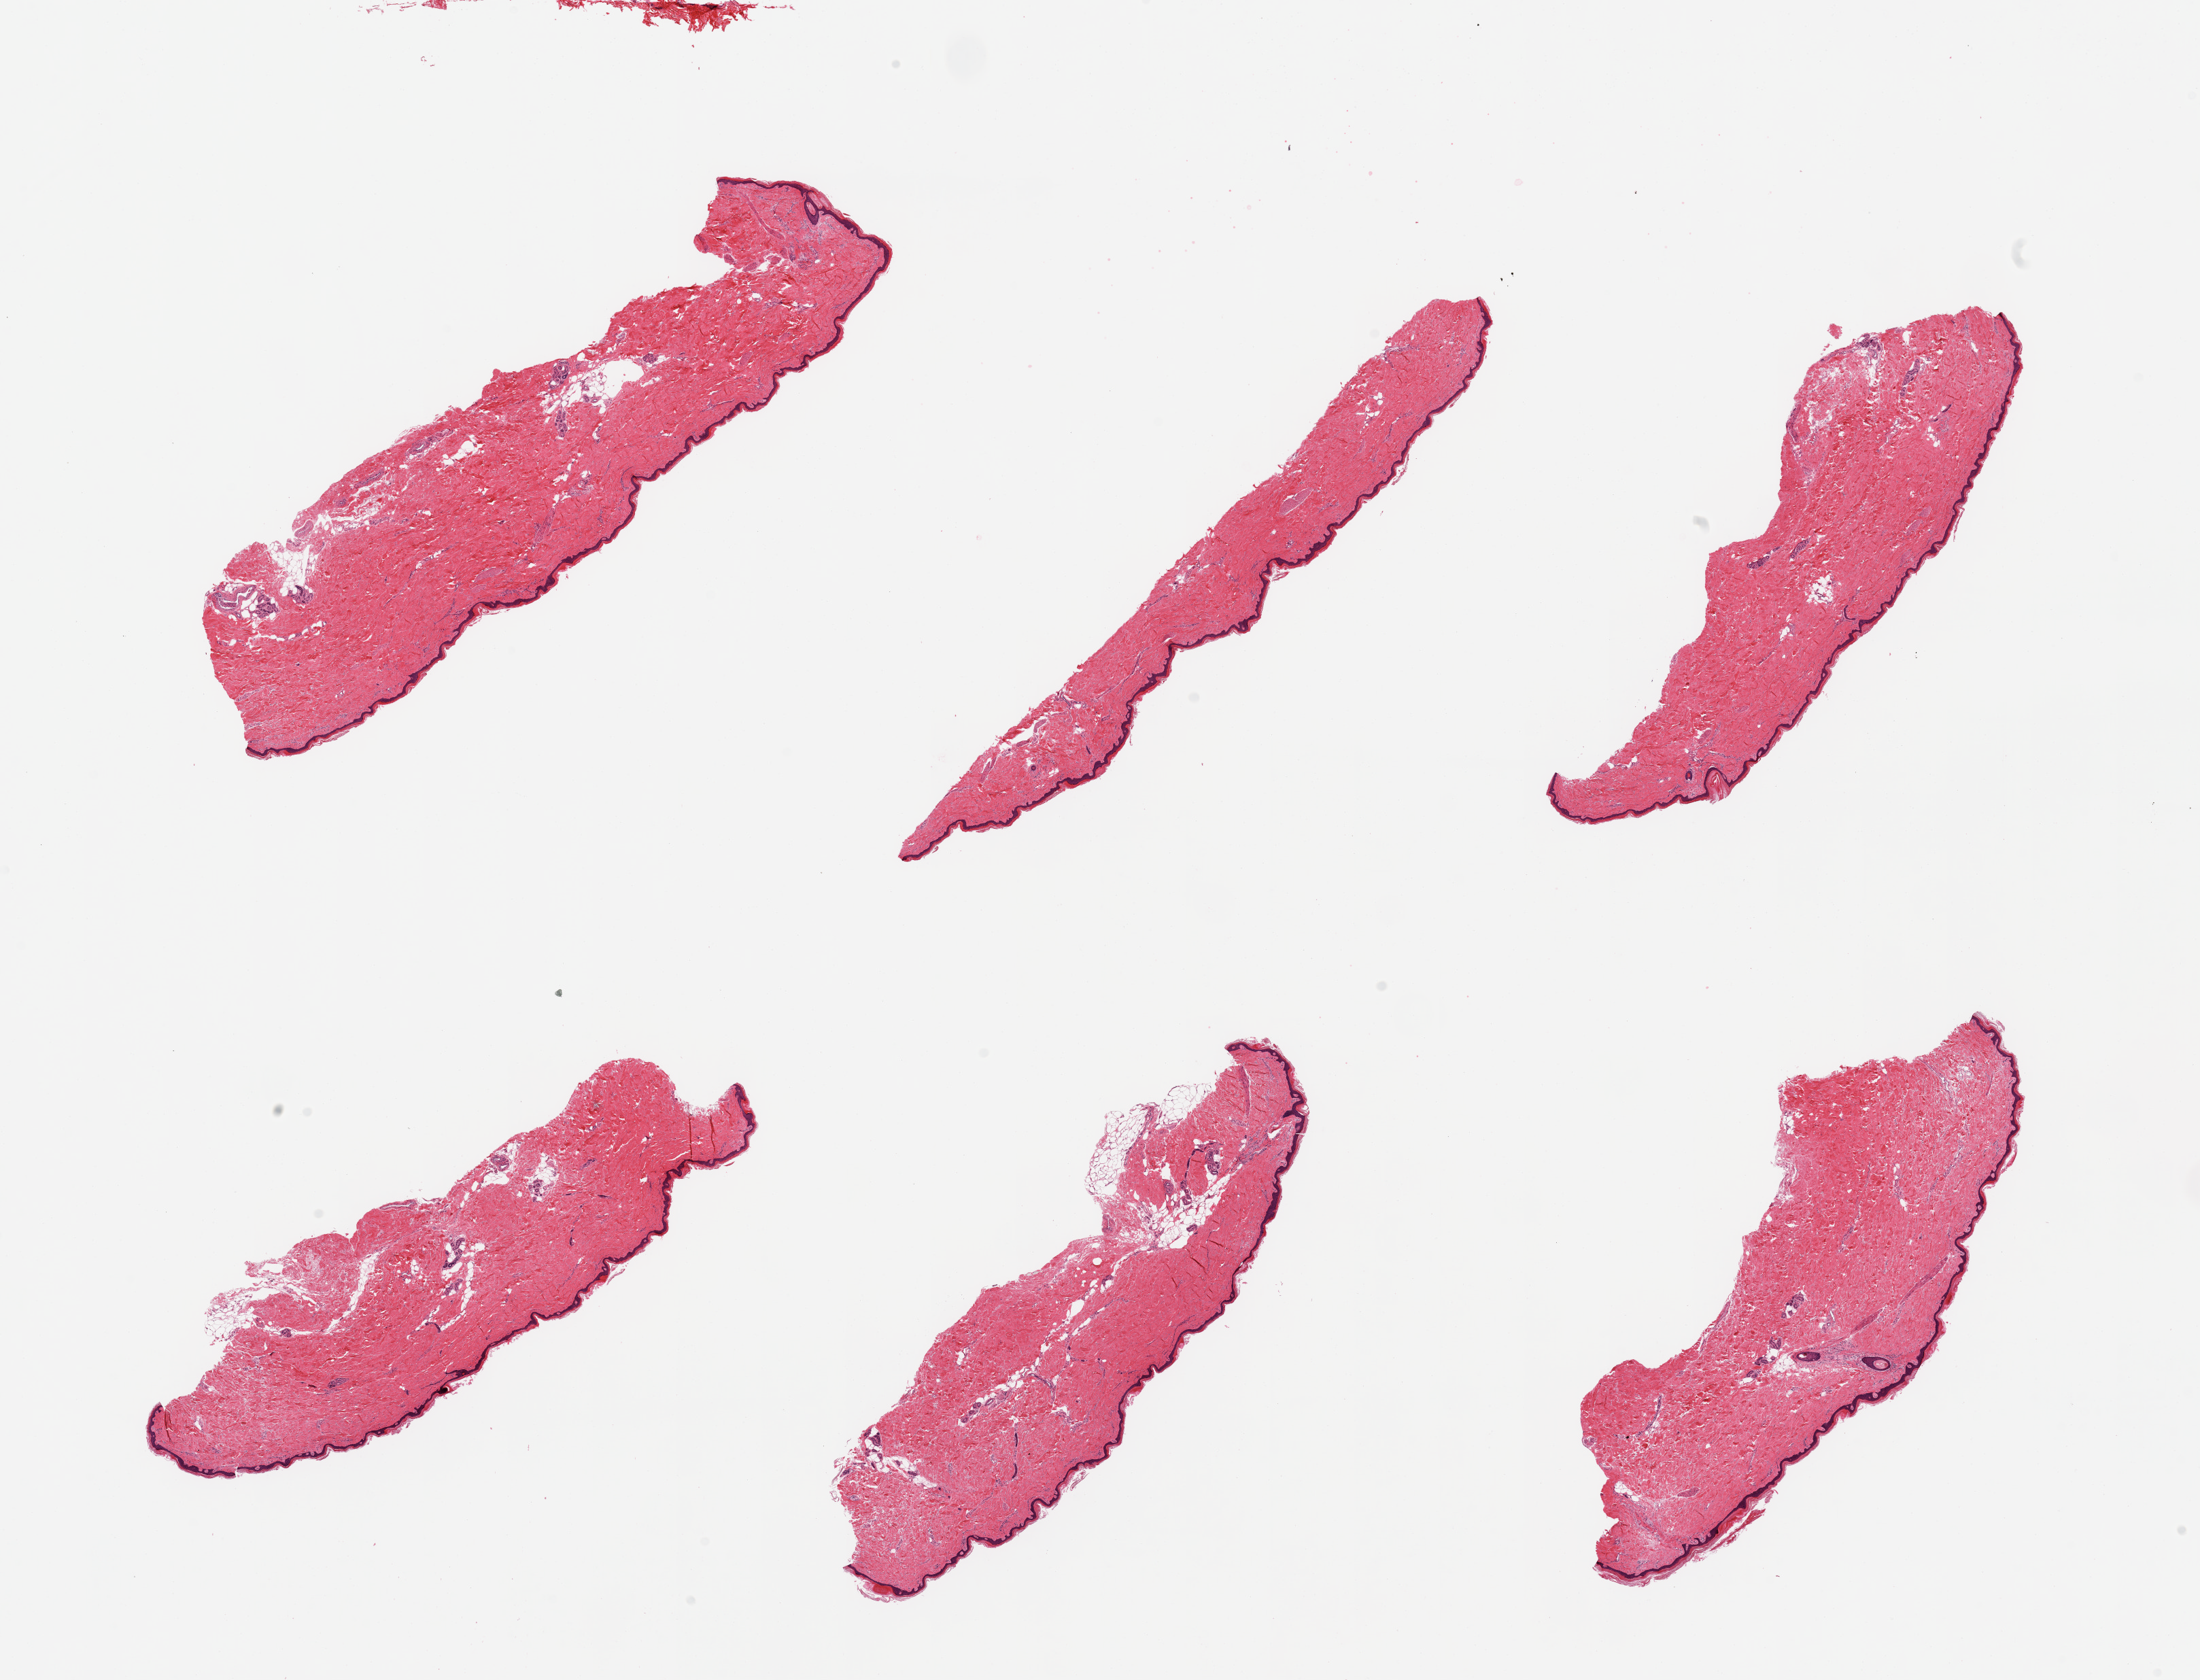
Digitized H&E-stained section, brightfield — a low-resolution overview of the entire scanned area, about 25.6 x 19.5 mm; PAXgene-fixed paraffin-embedded (PFPE) section; target tissue: skin of lower leg; tissue donor sample. Male donor.
Reviewer comment on this tissue sample: 6 pieces; predominantly well trimmed with minimal attached/internal fat, epidermis measures 31 microns.